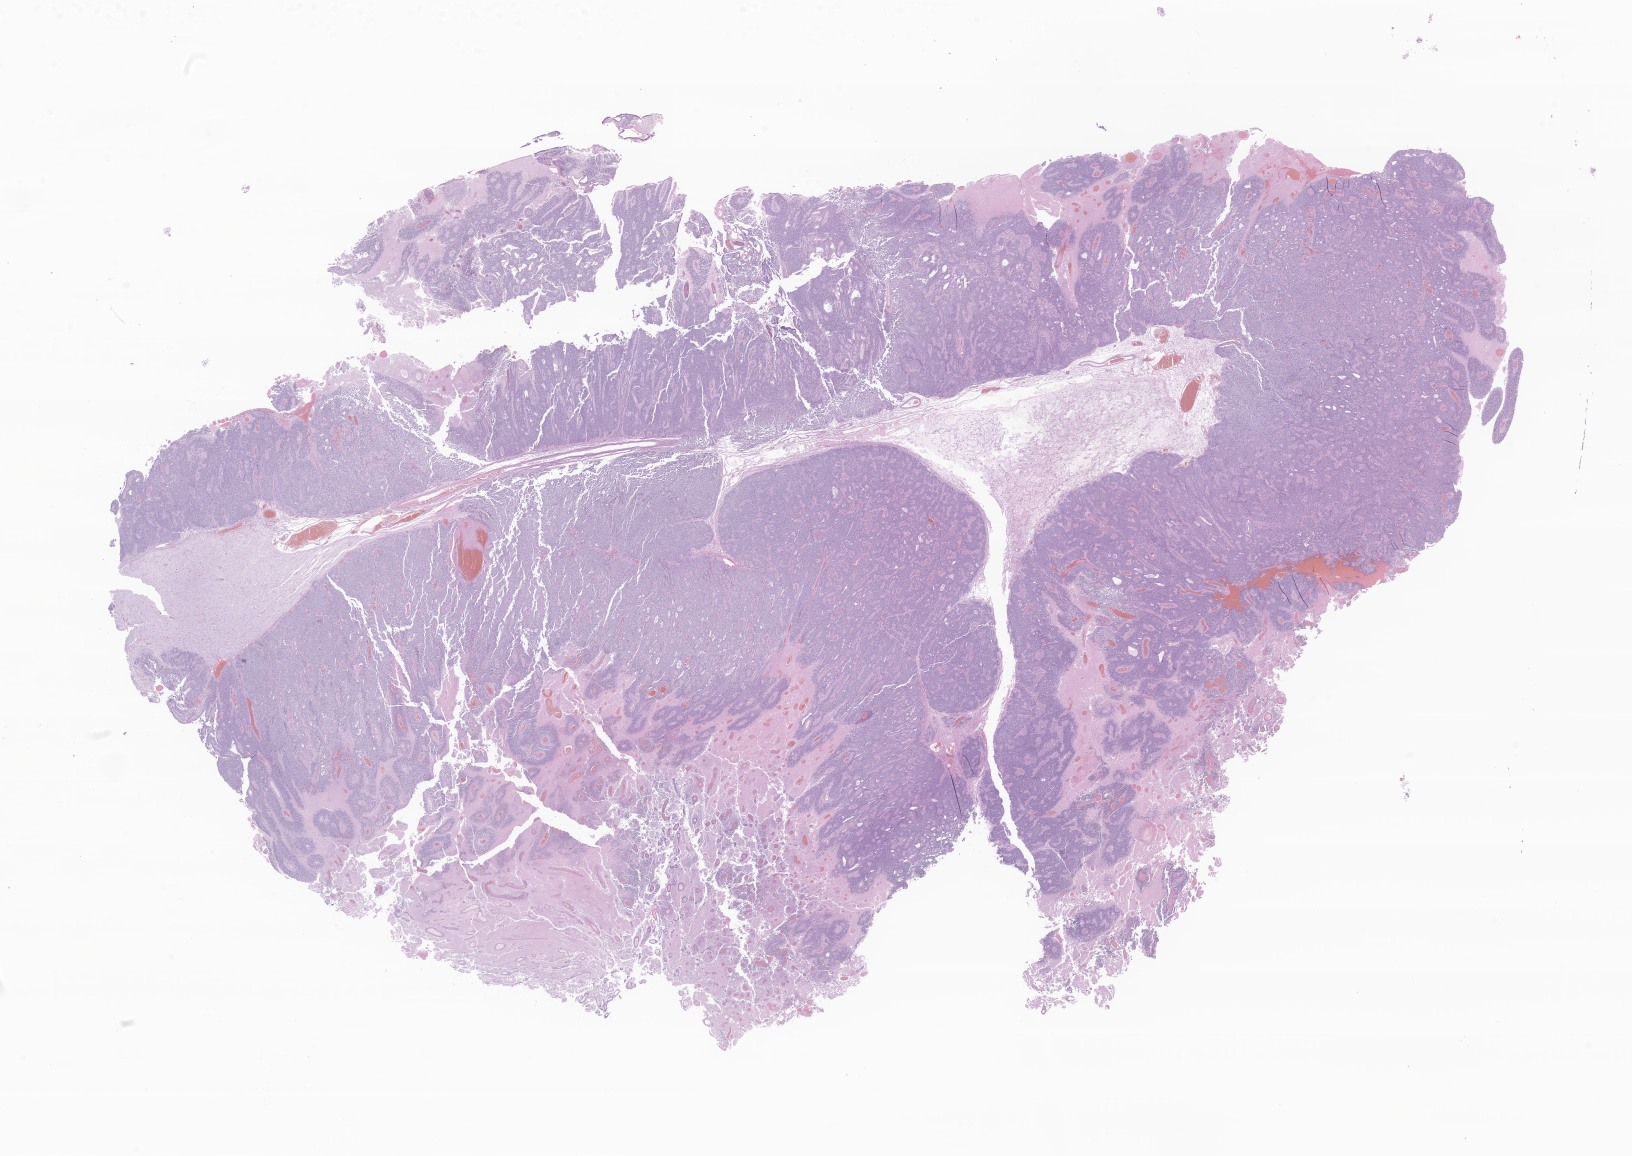
Digitized H&E-stained section of tumor tissue from the parietal lobe, shown as a low-resolution overview of the whole scanned area (about 27.5 x 19.5 mm), formalin-fixed paraffin-embedded section. Male patient, age 45 months (3 years 9 months).
• recorded diagnosis: Ependymoma, NOS